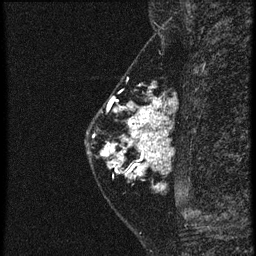
Breast MRI (dynamic contrast-enhanced), one sagittal slice; slice 22 of 60 in the series (ordered by position); 4 images stored at this slice position (order not interpretable as contrast timing); 1.5 T; TE 4.2 ms, TR 20.4 ms; 256 × 256 image matrix, field of view 180 × 180 mm. Patient: female, 46 years. From the clinical record (not read from this slice): setting: breast cancer imaged before/during neoadjuvant chemotherapy; receptor status: triple-negative.
Structures marked on this image (semi-automatically segmented with operator editing):
- analysis volume of interest (the breast-tissue region the enhancement analysis was run in; not a lesion): bounding box (x1, y1, x2, y2) in pixels: (88, 84, 167, 185)
- tumour enhancement mask (voxels above the 90 % enhancement threshold inside the analysis volume of interest): (102, 102, 167, 179)